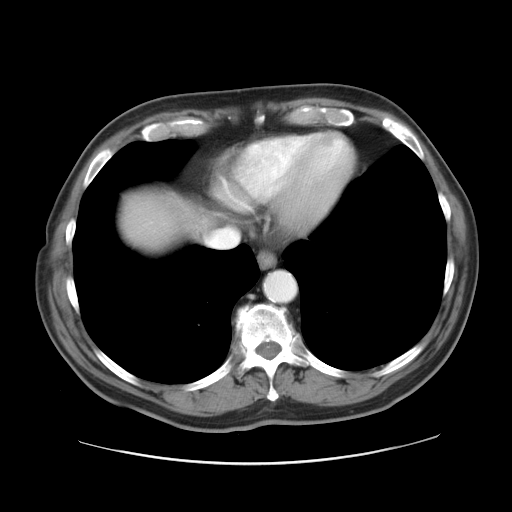
Contrast-enhanced abdominal CT, one axial slice; position 26 of 28 along the scan axis; reconstruction kernel STANDARD; 120 kVp; intravenous contrast given; soft-tissue window (W 400 / L 40 HU); 7.5 mm slice thickness; 512 × 512 image matrix, field of view 402 × 402 mm. Male patient, age 74 years. Case-level facts recorded for this patient, not image findings: diagnosis: colorectal cancer liver metastases, imaged before liver resection; multiple liver metastases: no; largest metastasis: 5 cm; chemotherapy before resection: yes.
Structures marked on this image (outlined manually by an expert reader):
- liver: bounding box (x1, y1, x2, y2) in pixels: (125, 200, 185, 247)
- planned liver remnant (the part of the liver to remain after resection): (125, 201, 181, 247)